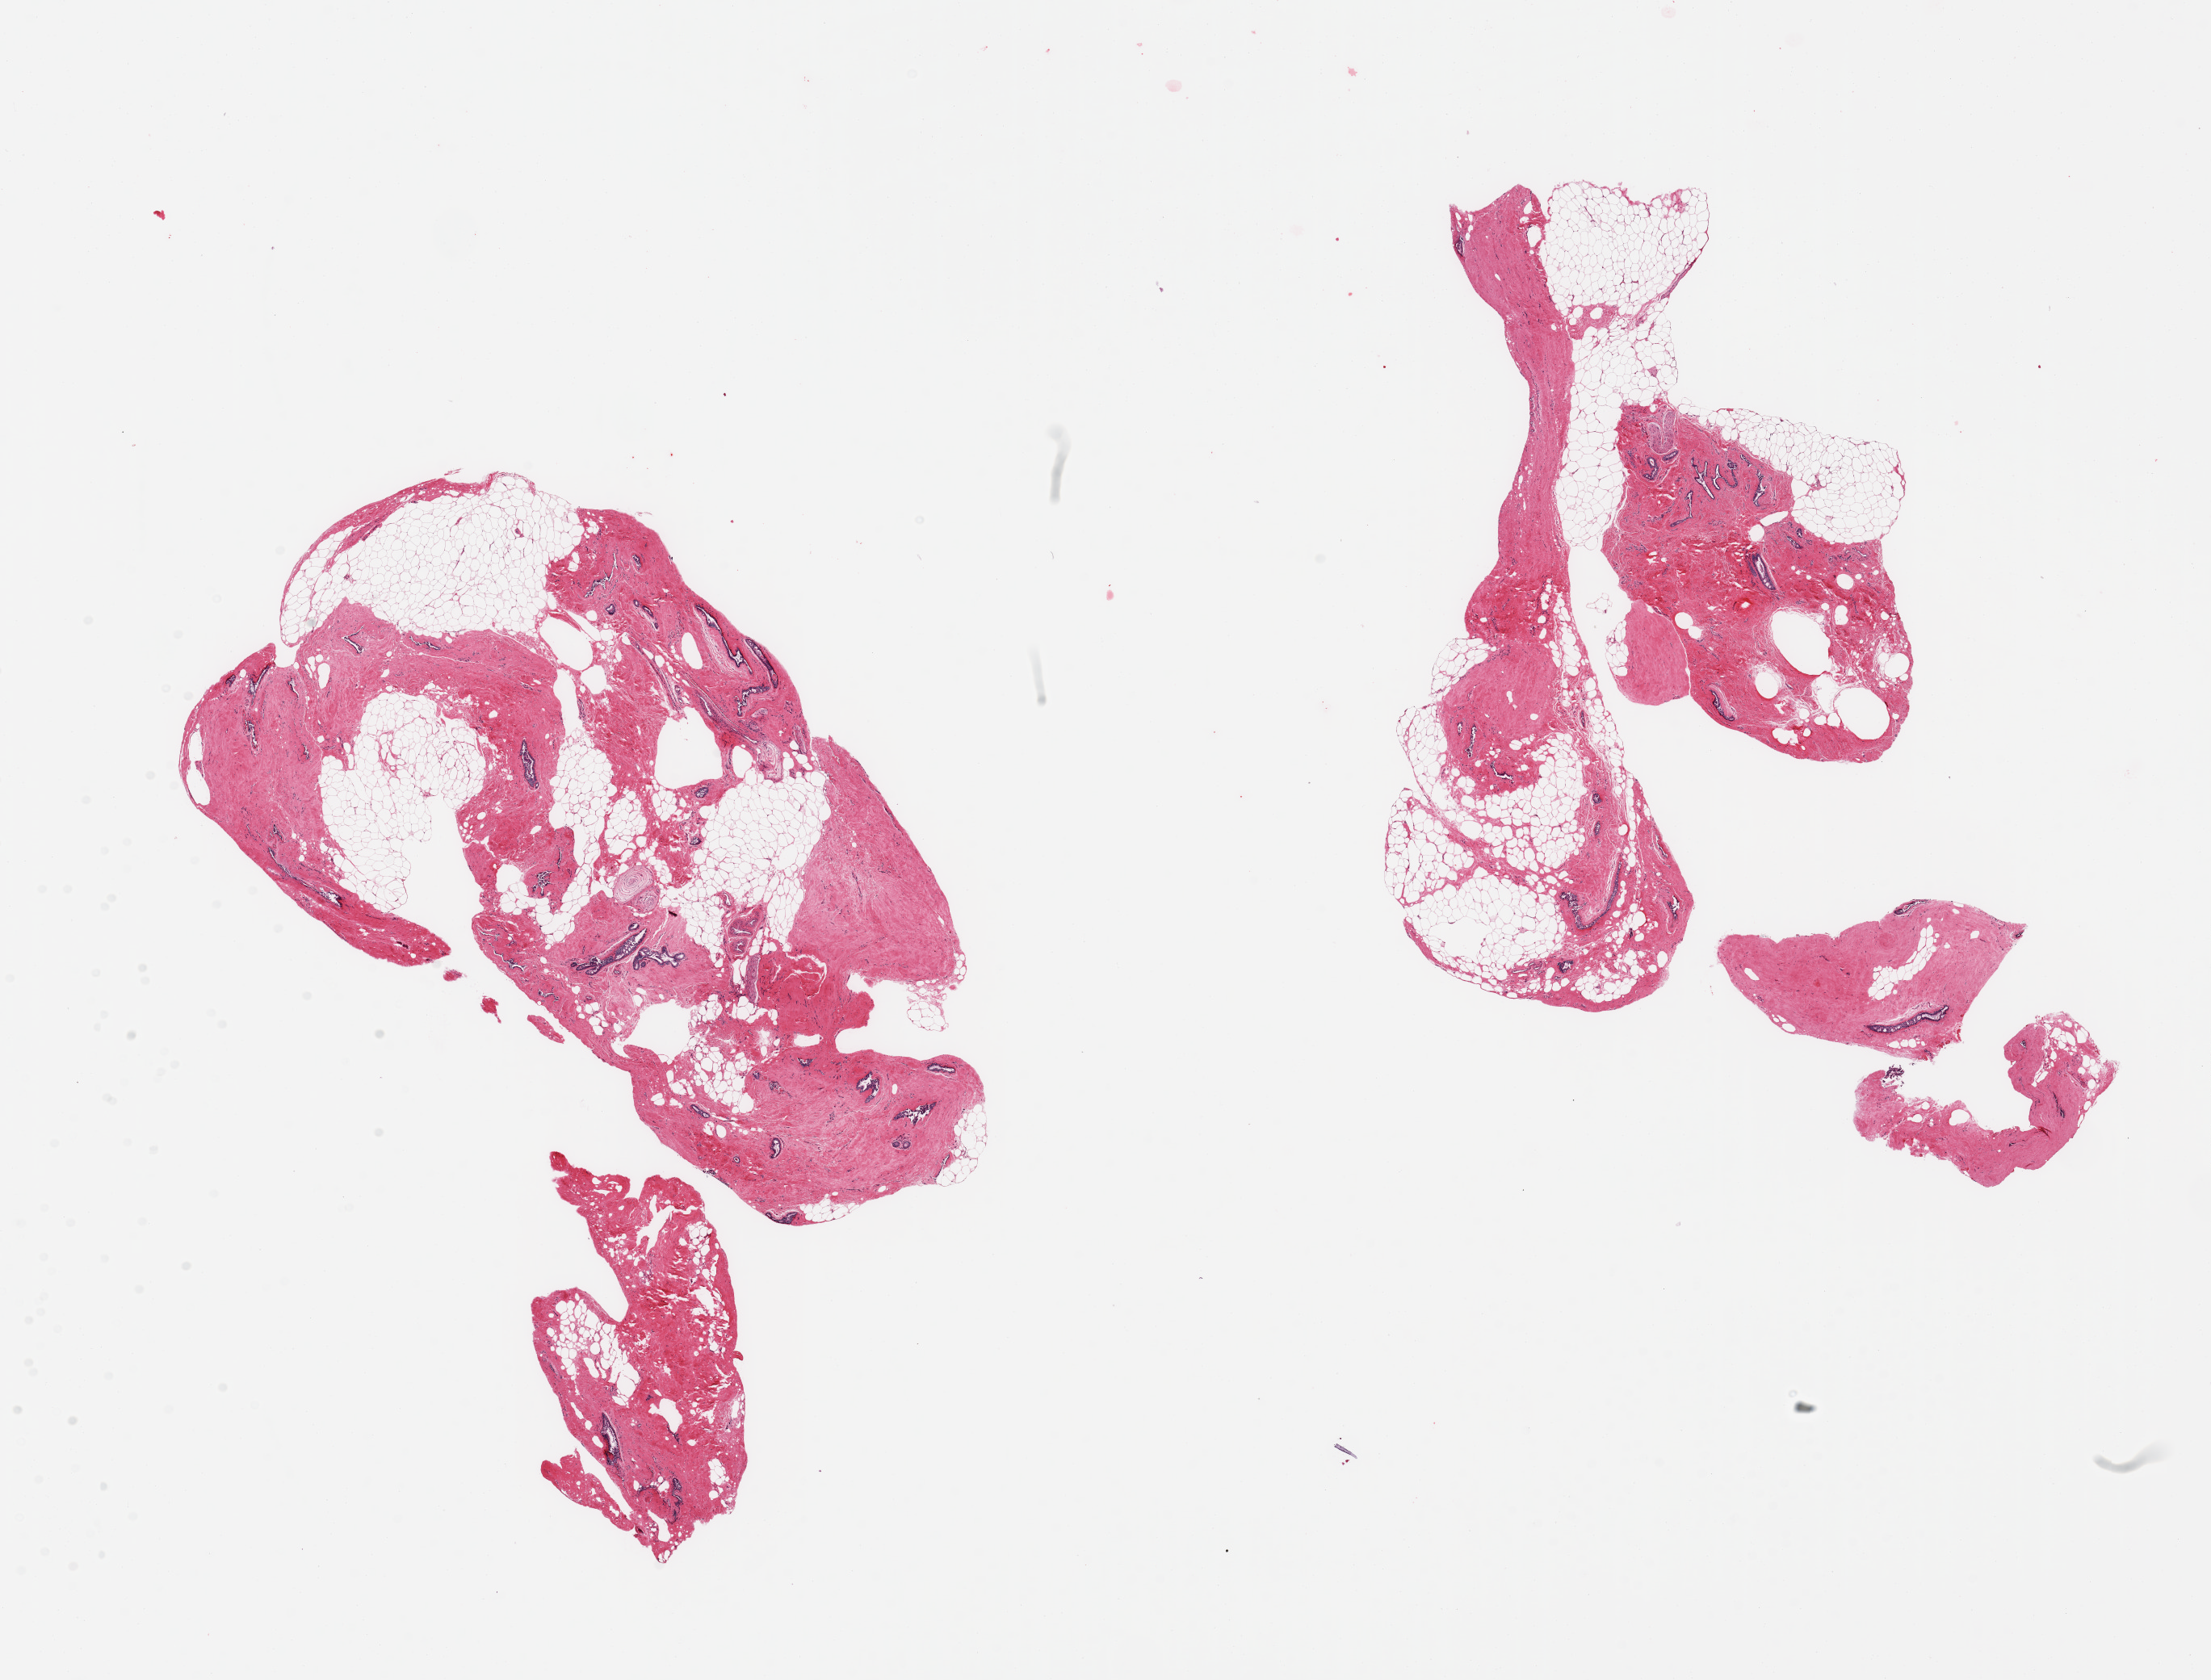
H&E whole-slide image — a low-resolution overview of the entire scanned area, about 21.7 x 16.5 mm (from a 20x scan), PAXgene-fixed, paraffin-embedded tissue, sampled site (target tissue): breast, donor tissue sample. Male donor.
Pathologist's review note for this sample: 2 pieces, stromal and ductal gynecomastoid hyperplasia; Pascinian corpuscle.